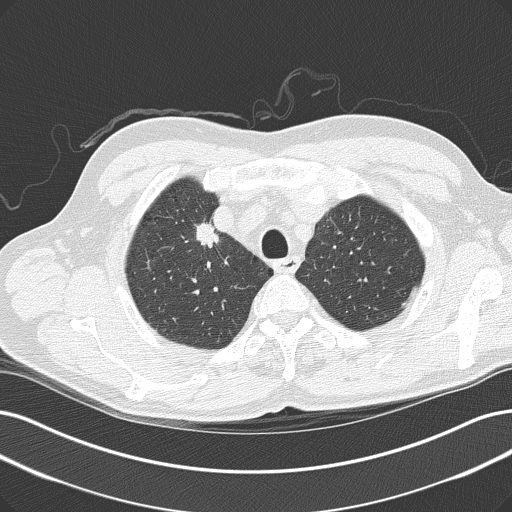
Chest CT (low-dose screening protocol), one axial image. Baseline screening round. Lung window (W 1500 / L -600 HU). Slice 30 of 152 in the series. 512 × 512 image matrix, field of view 365 × 365 mm. Male participant, aged 61 years at enrolment. Current smoker at enrolment.
Lesion marked by an expert reader, box from (x=190, y=221) to (x=246, y=268) px. The screening reader recorded 2 non-calcified nodules or masses ≥4 mm on this exam (right upper lobe, right upper lobe); which of them this box marks is not recorded. Lung cancer was diagnosed 54 days after this screen: adenocarcinoma, NOS, right upper lobe, poorly differentiated (G3), stage IIIB (AJCC 6th edition).